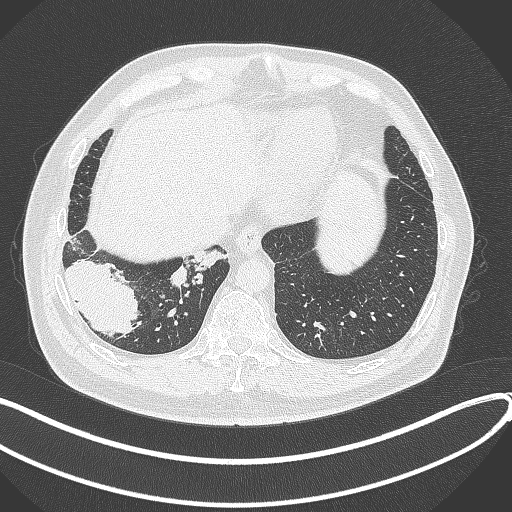
Chest CT, one axial slice; position 73 of 360 along the scan axis; 120 kVp; lung window (W 1500 / L -600 HU); 1 mm slice thickness; 512 × 512 image matrix, field of view 400 × 400 mm. Male patient, age 59 years.
Outlined on this slice (rectangle marked by the reading radiologist):
- lung tumour (recorded histology: adenocarcinoma): bounding box (x1, y1, x2, y2) in pixels: (66, 256, 139, 339)